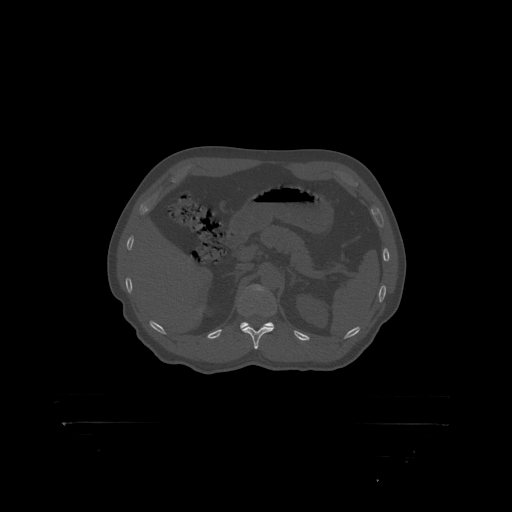
CT including the spine, one axial slice. Position 342 of 399 along the scan axis. Reconstruction kernel STANDARD. 120 kVp. Bone window (W 1800 / L 400 HU). 1.25 mm slice thickness. 512 × 512 image matrix, field of view 650 × 650 mm. Patient: male, 46 years. Case-level facts recorded for this patient, not image findings: primary cancer: skin.
Outlined on this slice (semi-automatic segmentation, software-assisted and operator-edited):
- L1 vertebra: bounding box [x1, y1, x2, y2] px = [245, 285, 269, 297]